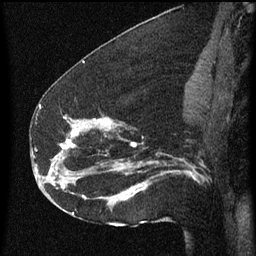
Breast MRI (dynamic contrast-enhanced), one sagittal slice. Position 33 of 60 along the scan axis. Dynamic contrast-enhanced series, image 2 of 3 at this slice position (ordered by acquisition). 1.5 T. TE 4.2 ms, TR 8 ms. 2 mm slice thickness. 256 × 256 image matrix. Female patient, age 52 years.
Annotated regions visible in this slice (semi-automatically segmented with operator editing):
- analysis volume of interest (the breast-tissue region the enhancement analysis was run in; not a lesion): box from (x=54, y=110) to (x=178, y=207) px
- tumour enhancement mask (voxels above the 70 % enhancement threshold inside the analysis volume of interest): (x=60, y=118)–(x=148, y=201)